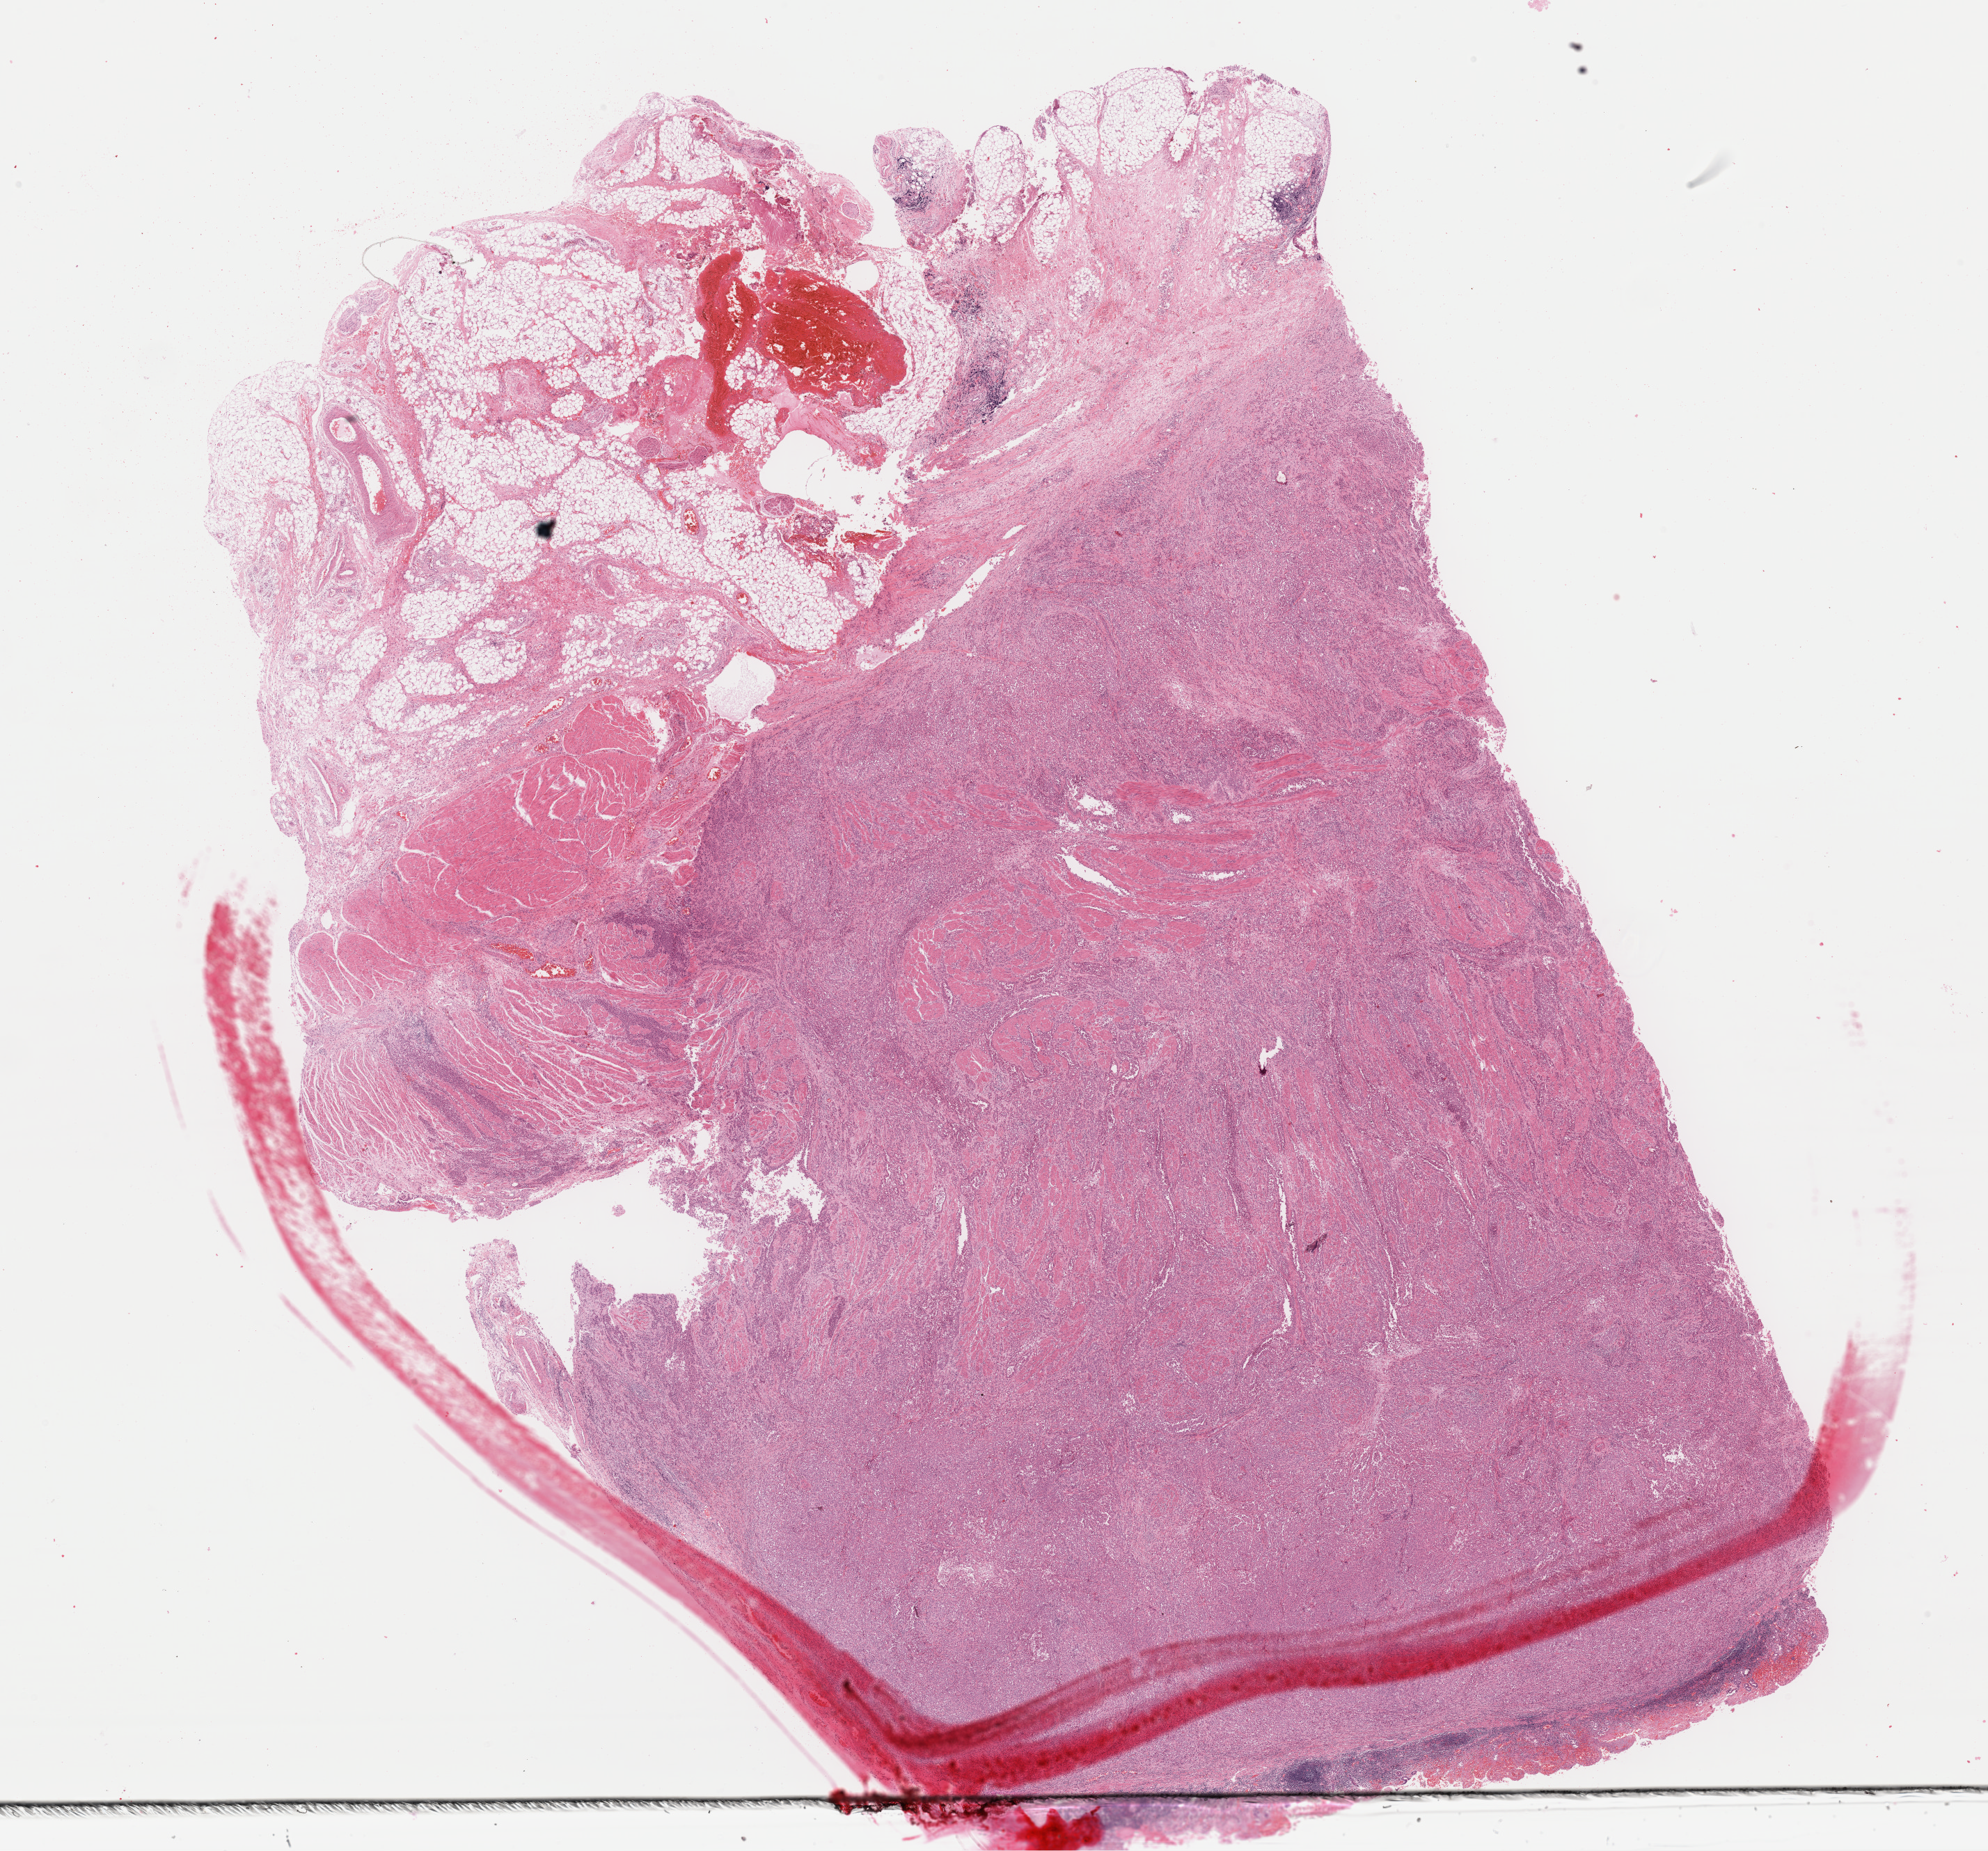
Digitized Hematoxylin and eosin (H&E) stained tissue section (whole slide) — shown as a low-resolution overview of the whole scanned area (about 22.6 x 21.0 mm, slide scanned at 40x), FFPE section, primary tumour sample from the stomach. Male, age 39 years at initial diagnosis. Histologic grade: G3 (poorly differentiated).
- AJCC pathologic stage: IIIB (7th edition)
- pathologic diagnosis: Adenocarcinoma, NOS